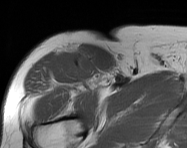
MRI of an extremity soft-tissue mass, one axial slice; position 111 of 114 along the scan axis; MR volume resampled by the dataset authors to the PET/CT grid (not the native acquisition matrix); 3.27 mm slice thickness; 187 × 148 image matrix, field of view 183 × 145 mm. Male patient. From the clinical record (not read from this slice): histological type: pleiomorphic leiomyosarcoma; grade: intermediate; site of the primary tumour: right thigh.
Structures marked on this image (expert contour drawn on MRI and transferred to this co-registered scan by the dataset authors):
- gross tumour volume including surrounding oedema: bounding box <73,52,99,82> (left, top, right, bottom; pixels)